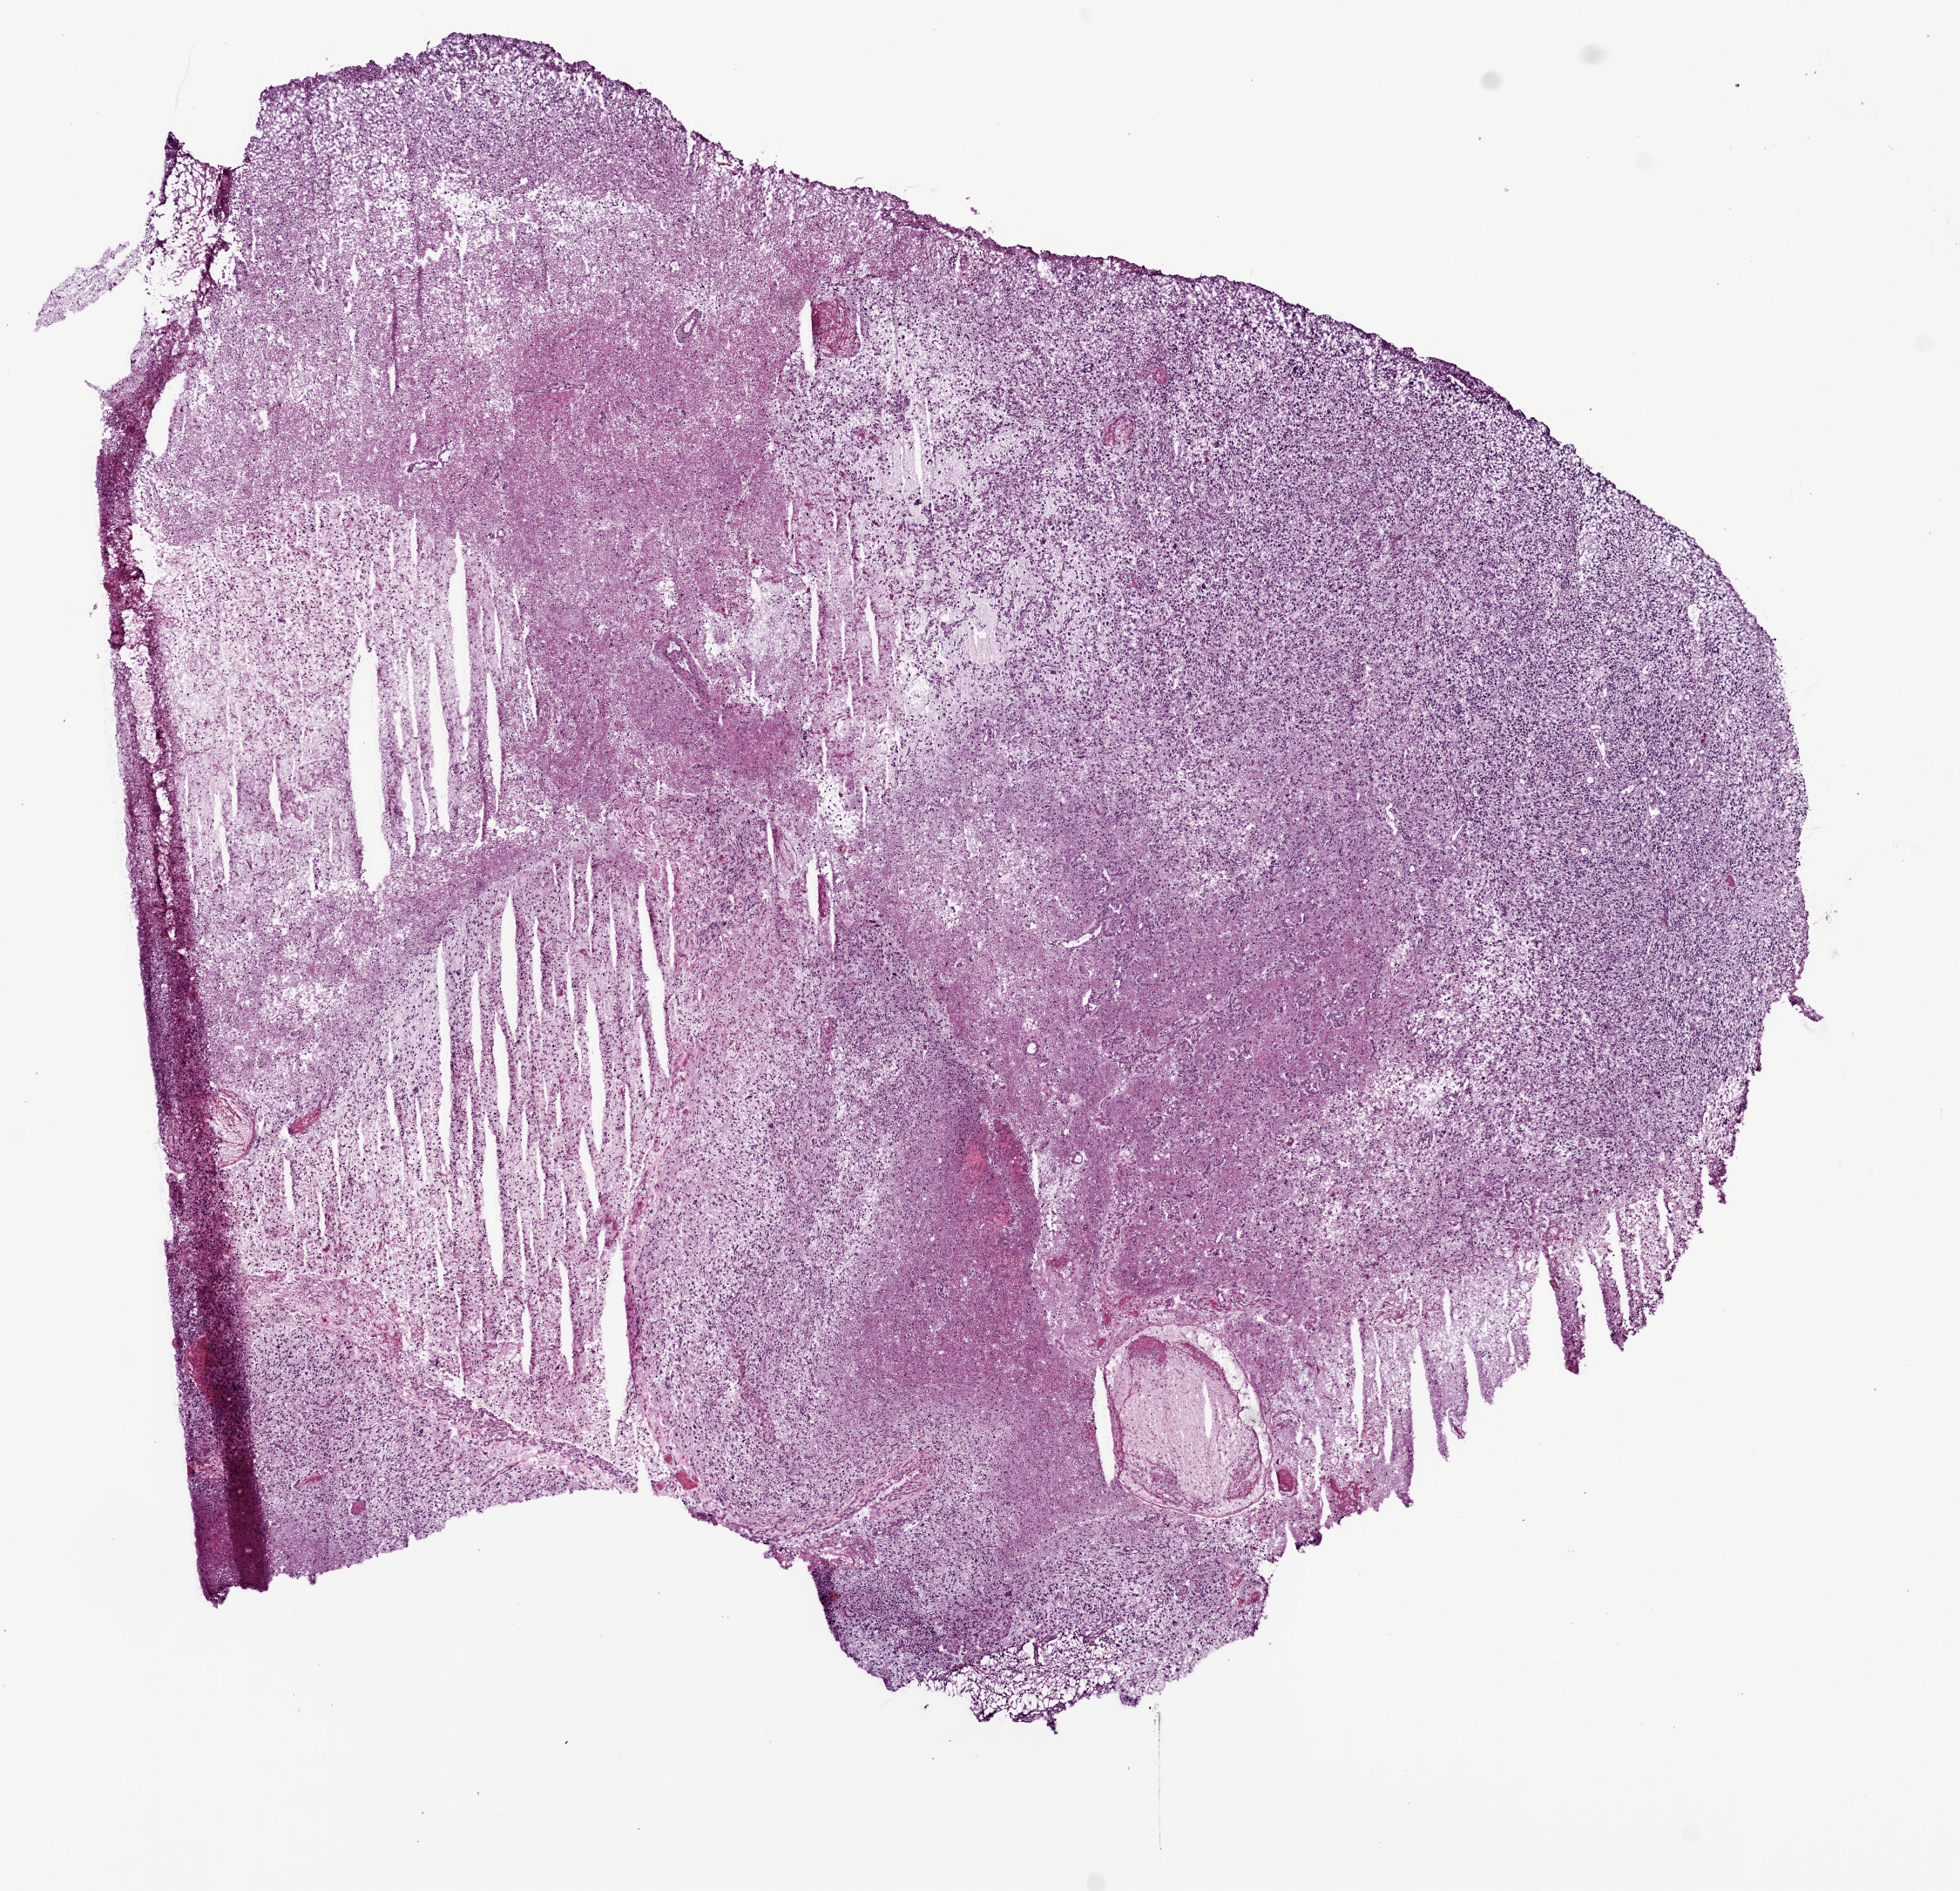
Digitized H&E tissue section (whole slide) — low-resolution overview of the scanned area, about 9.0 x 8.7 mm (acquisition: 20x scan); frozen section from the bottom of the tissue portion; brain, primary tumour sample. Patient: male, age at initial diagnosis 53 years. Composition of this section per pathologist review: tumour cells 100%, tumour nuclei 75%, normal cells 0%, stromal cells 0%, necrosis 0%.
* diagnosis: Glioblastoma